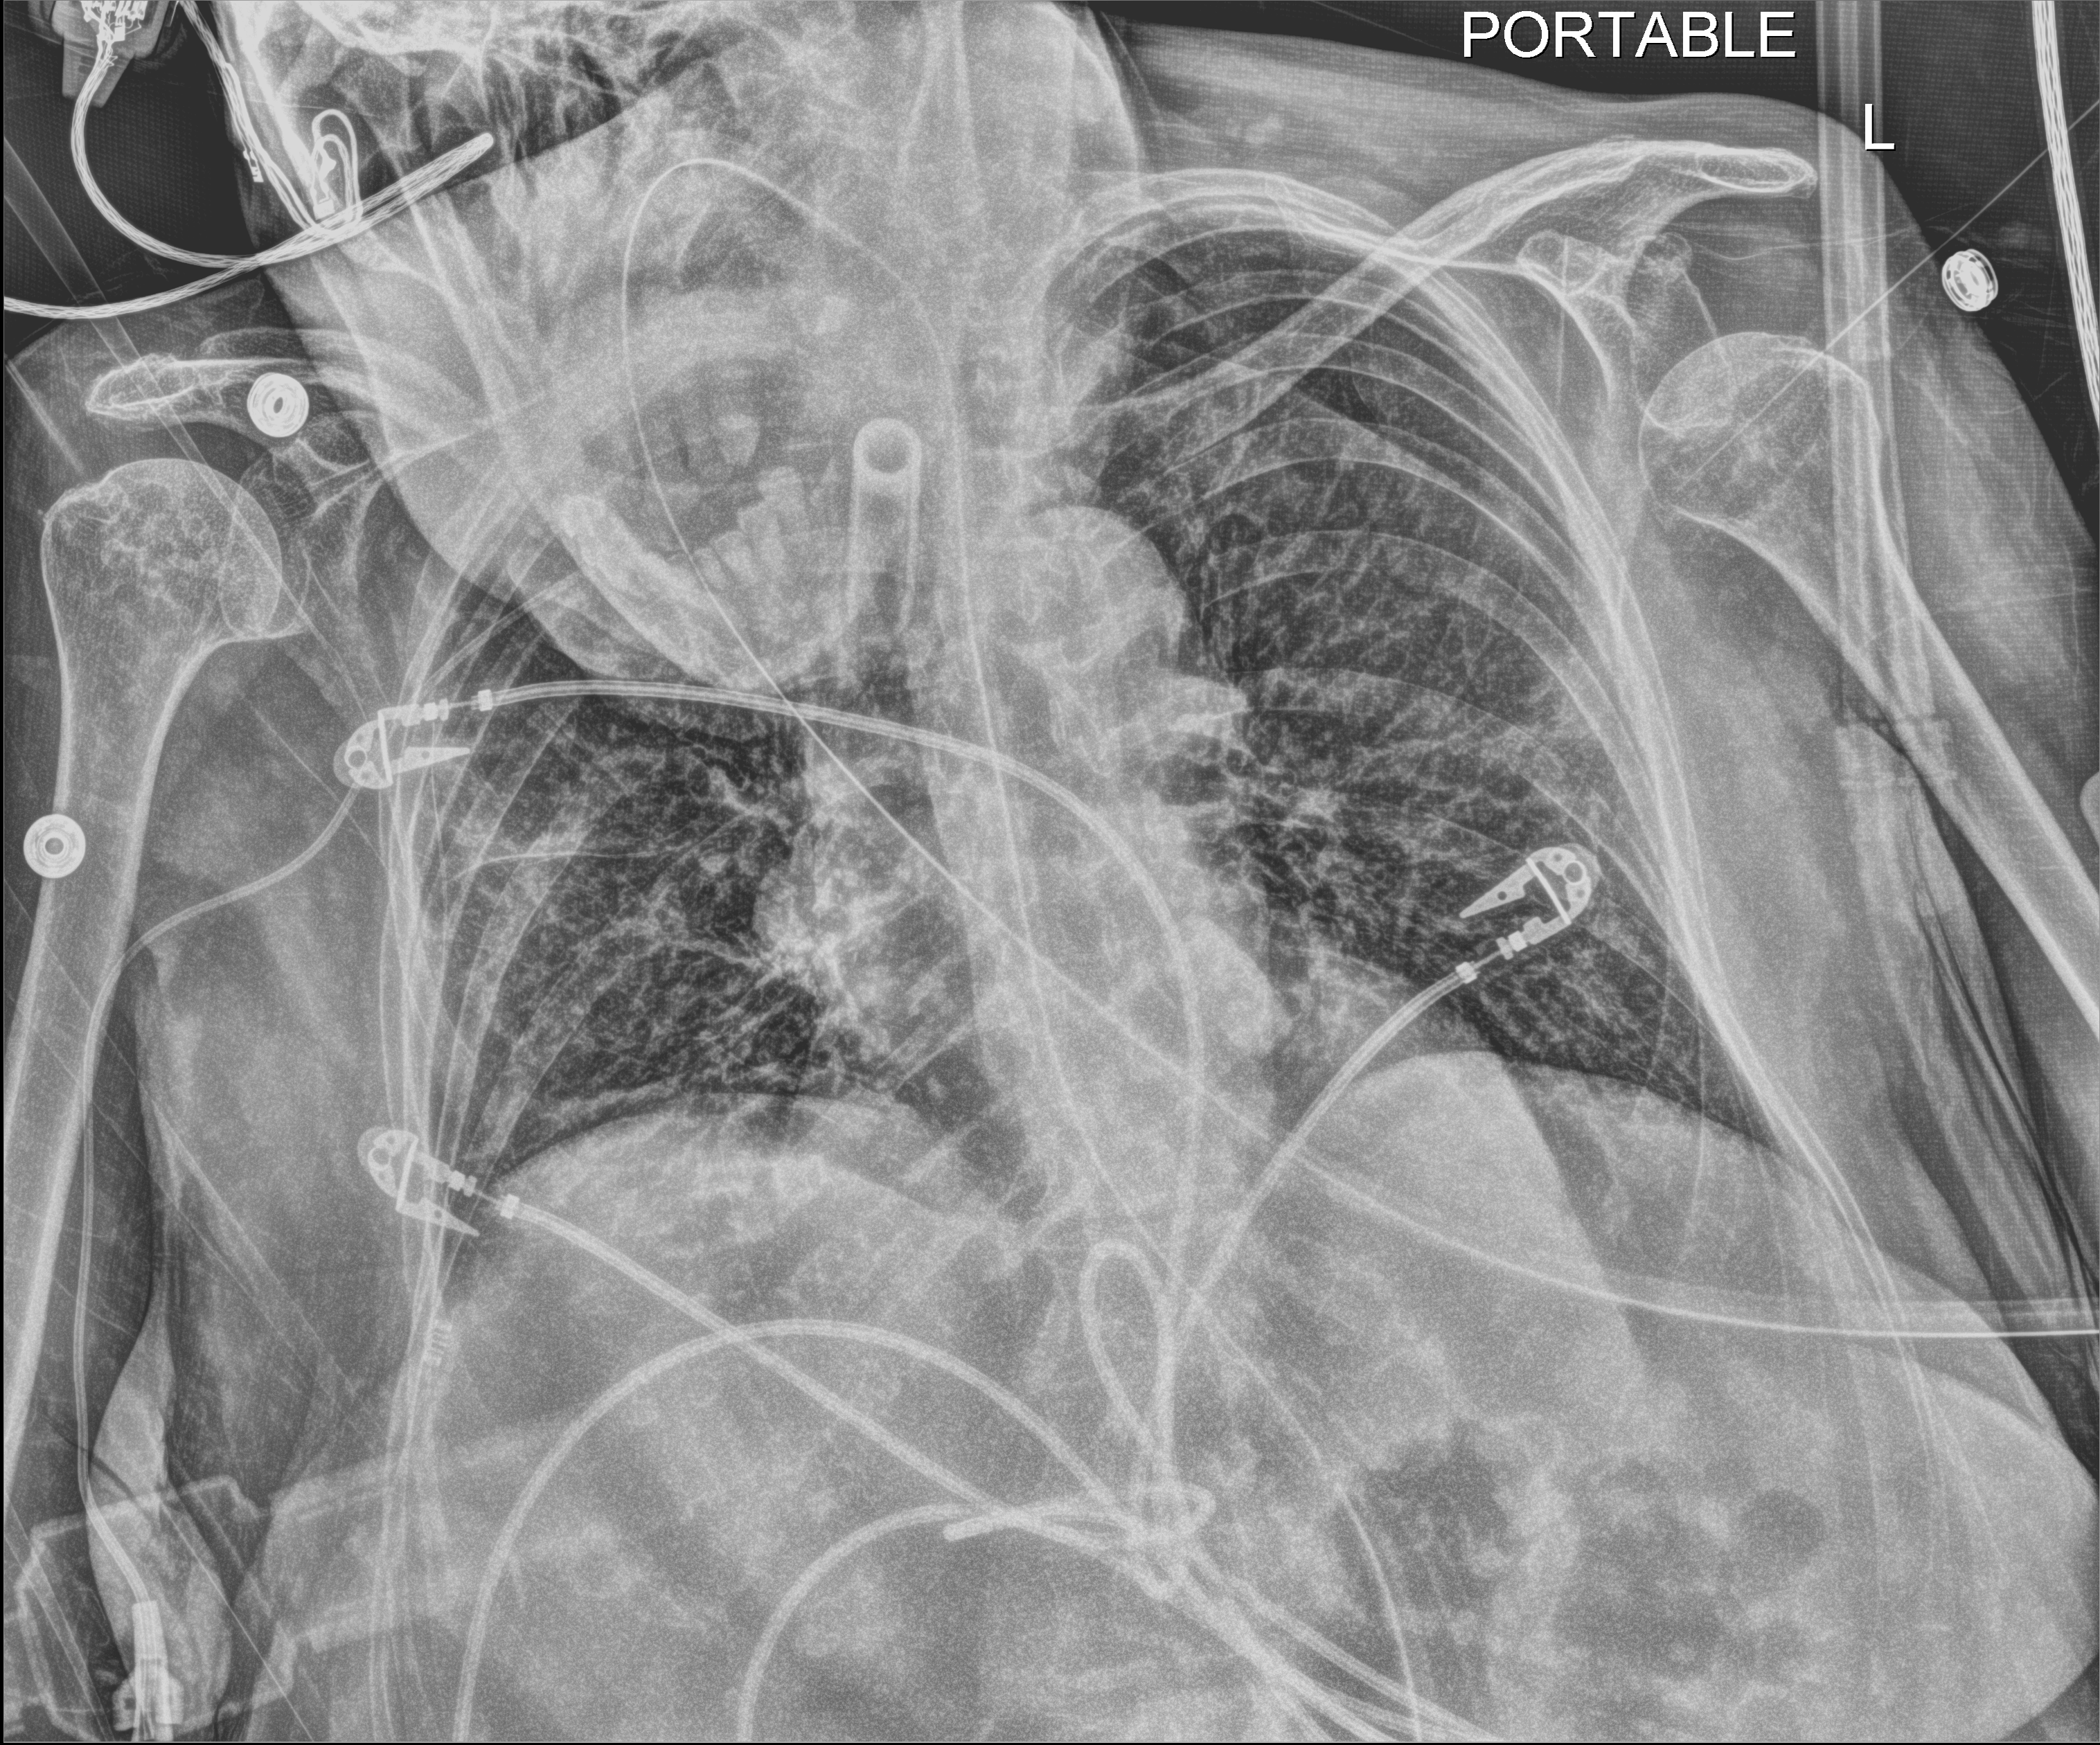
Chest X-ray (portable); anteroposterior (AP) projection. Female patient hospitalised with COVID-19, age 75–90 years.
Hospital-stay facts (about this admission, not read from this image; timing relative to this image not recorded):
- smoking status (admission record): former
- admitted to intensive care during this hospital stay: yes
- mechanically ventilated during this hospital stay: yes